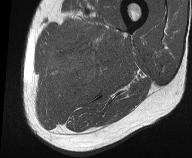
MRI of an extremity soft-tissue mass, one axial slice. Slice 15 of 61 in the series (ordered by position). MR volume resampled by the dataset authors to the PET/CT grid (not the native acquisition matrix). 3.27 mm slice thickness. 192 × 158 image matrix, field of view 187 × 154 mm. Male patient. From the clinical record (not read from this slice): histological type: pleiomorphic liposarcoma; grade: high; site of the primary tumour: left thigh.
Annotated regions visible in this slice (expert contour drawn on MRI and transferred to this co-registered scan by the dataset authors):
- gross tumour volume including surrounding oedema: bounding box [x1, y1, x2, y2] px = [50, 18, 119, 95]
- gross tumour volume (mass): [57, 55, 103, 90]